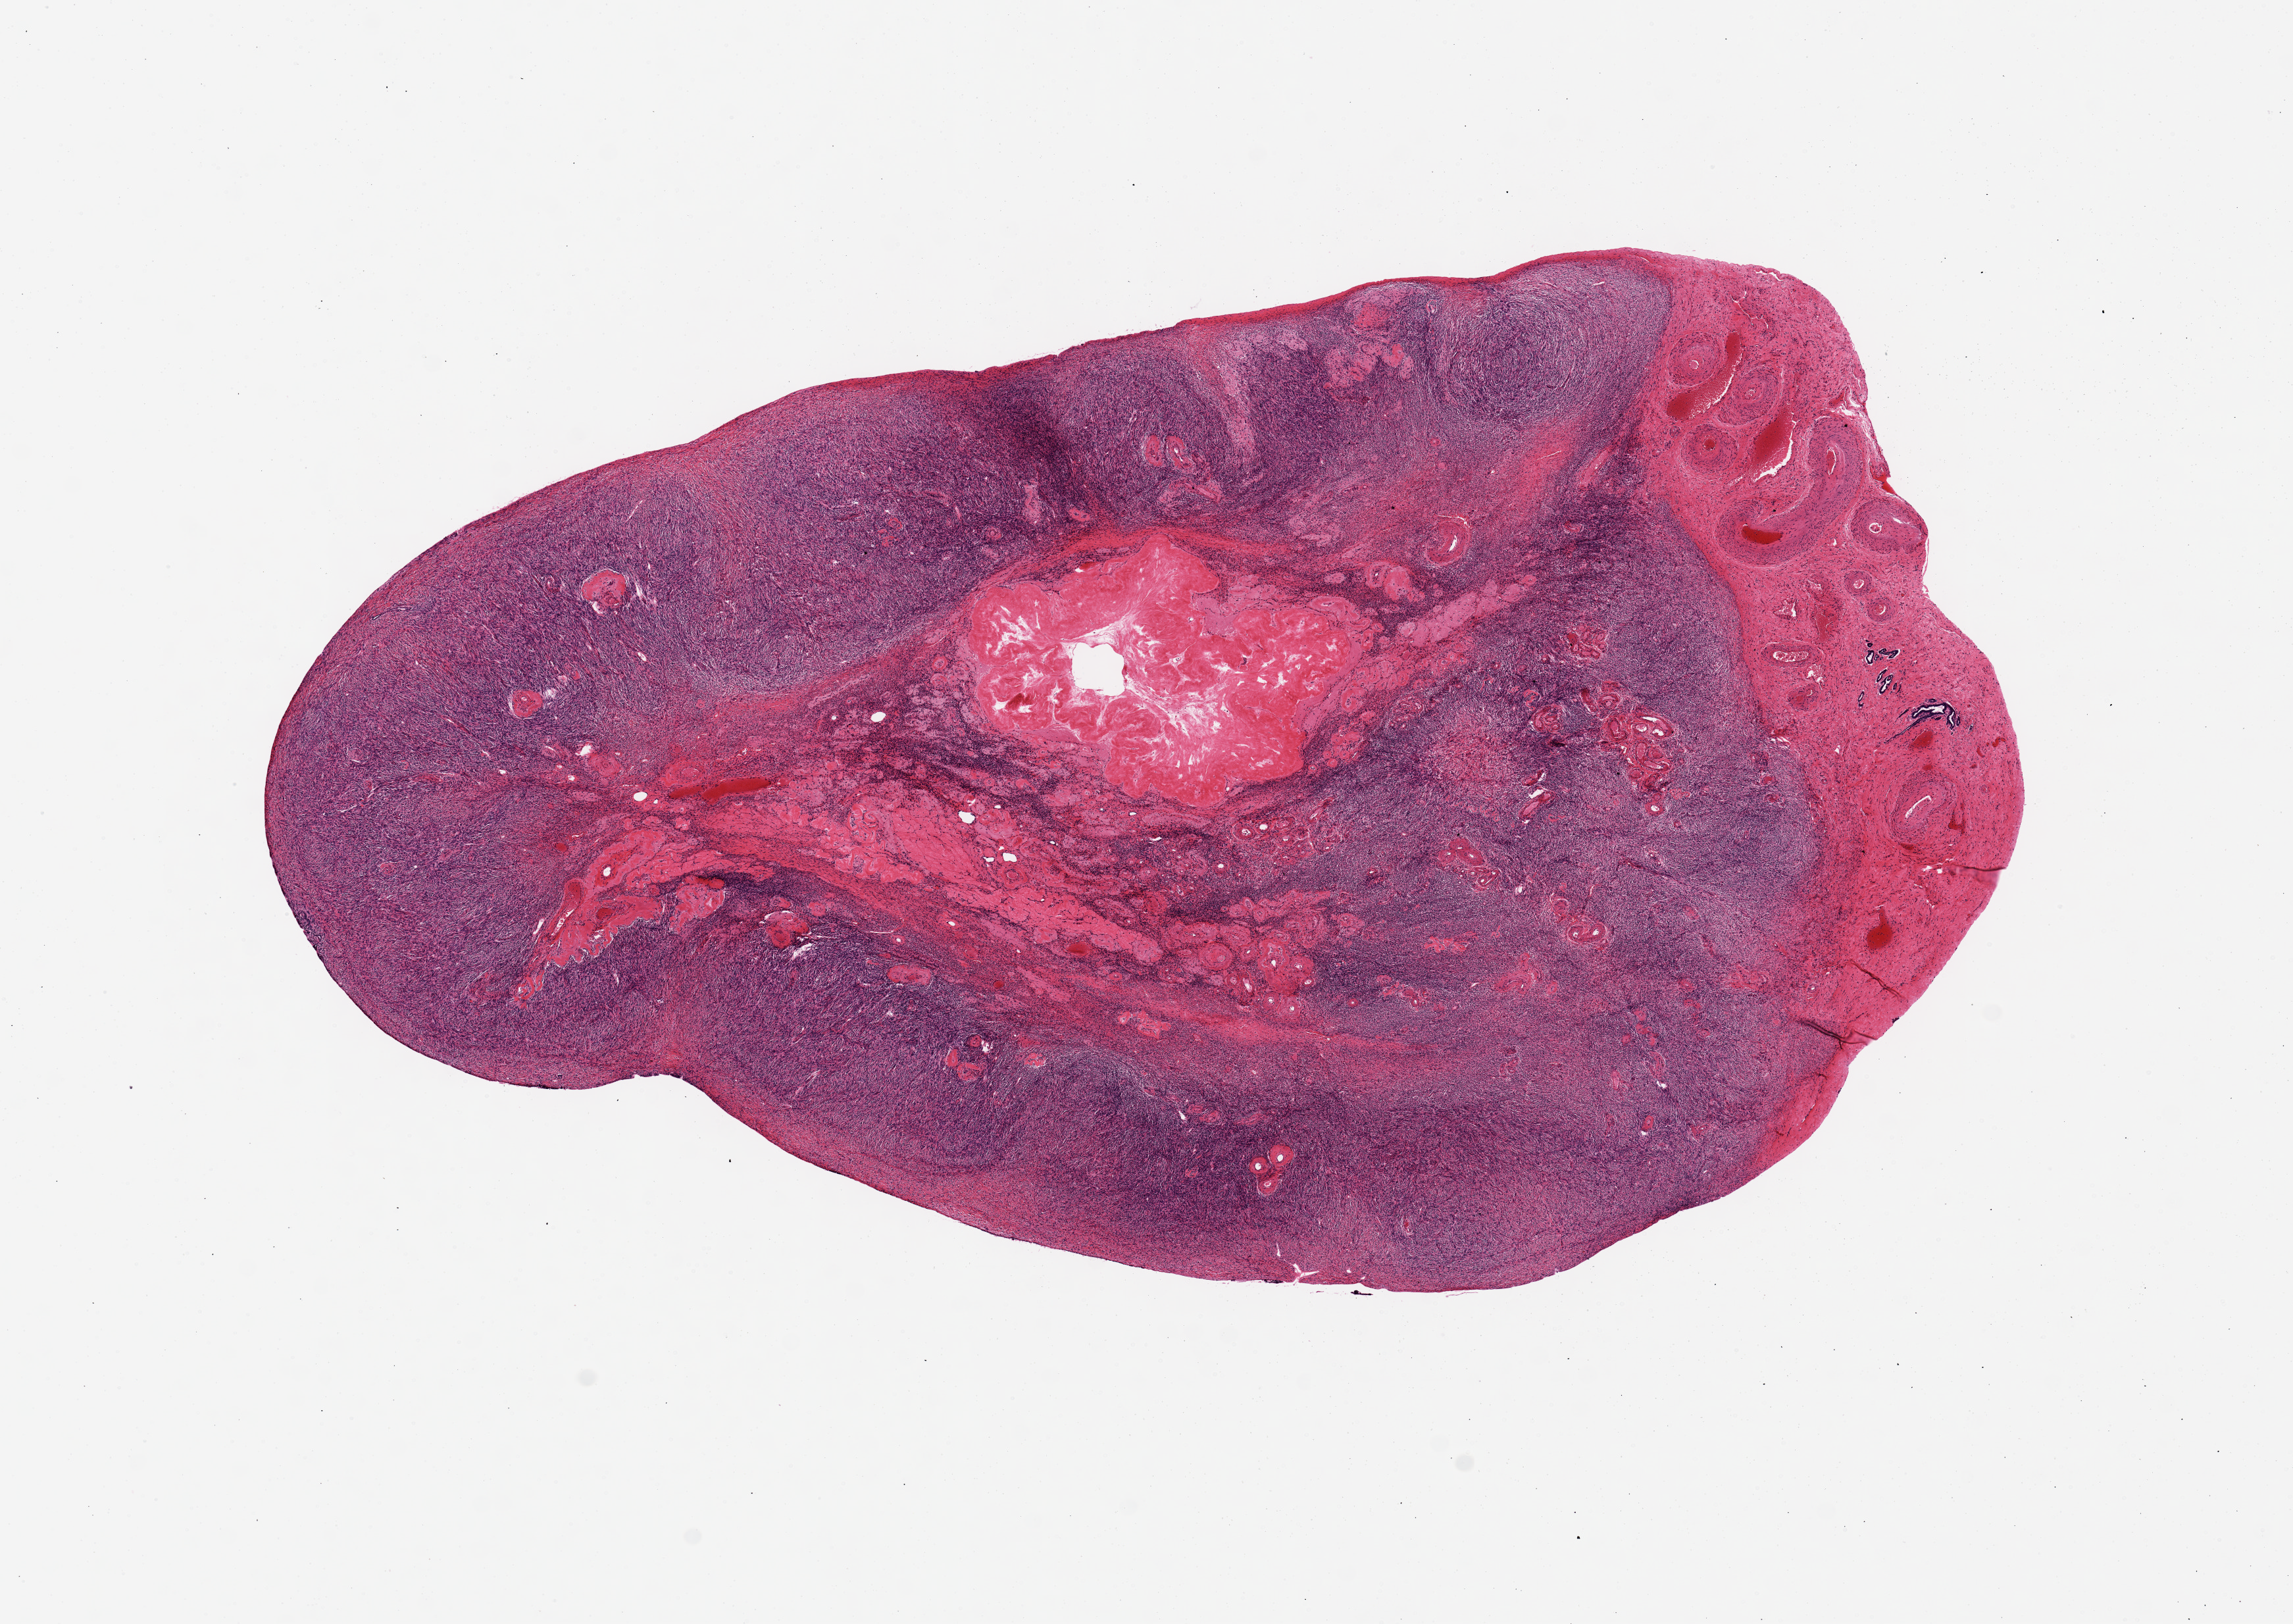
Whole-slide image, haematoxylin and eosin stain, low-resolution overview of the scanned area, about 13.8 x 9.8 mm (from a 20x scan), PAXgene-fixed paraffin-embedded (PFPE) section, section of ovary (target tissue), tissue donor sample. Donor: female.
Reviewer comment on this tissue sample: Well-preserved; post menopausal/inactive.